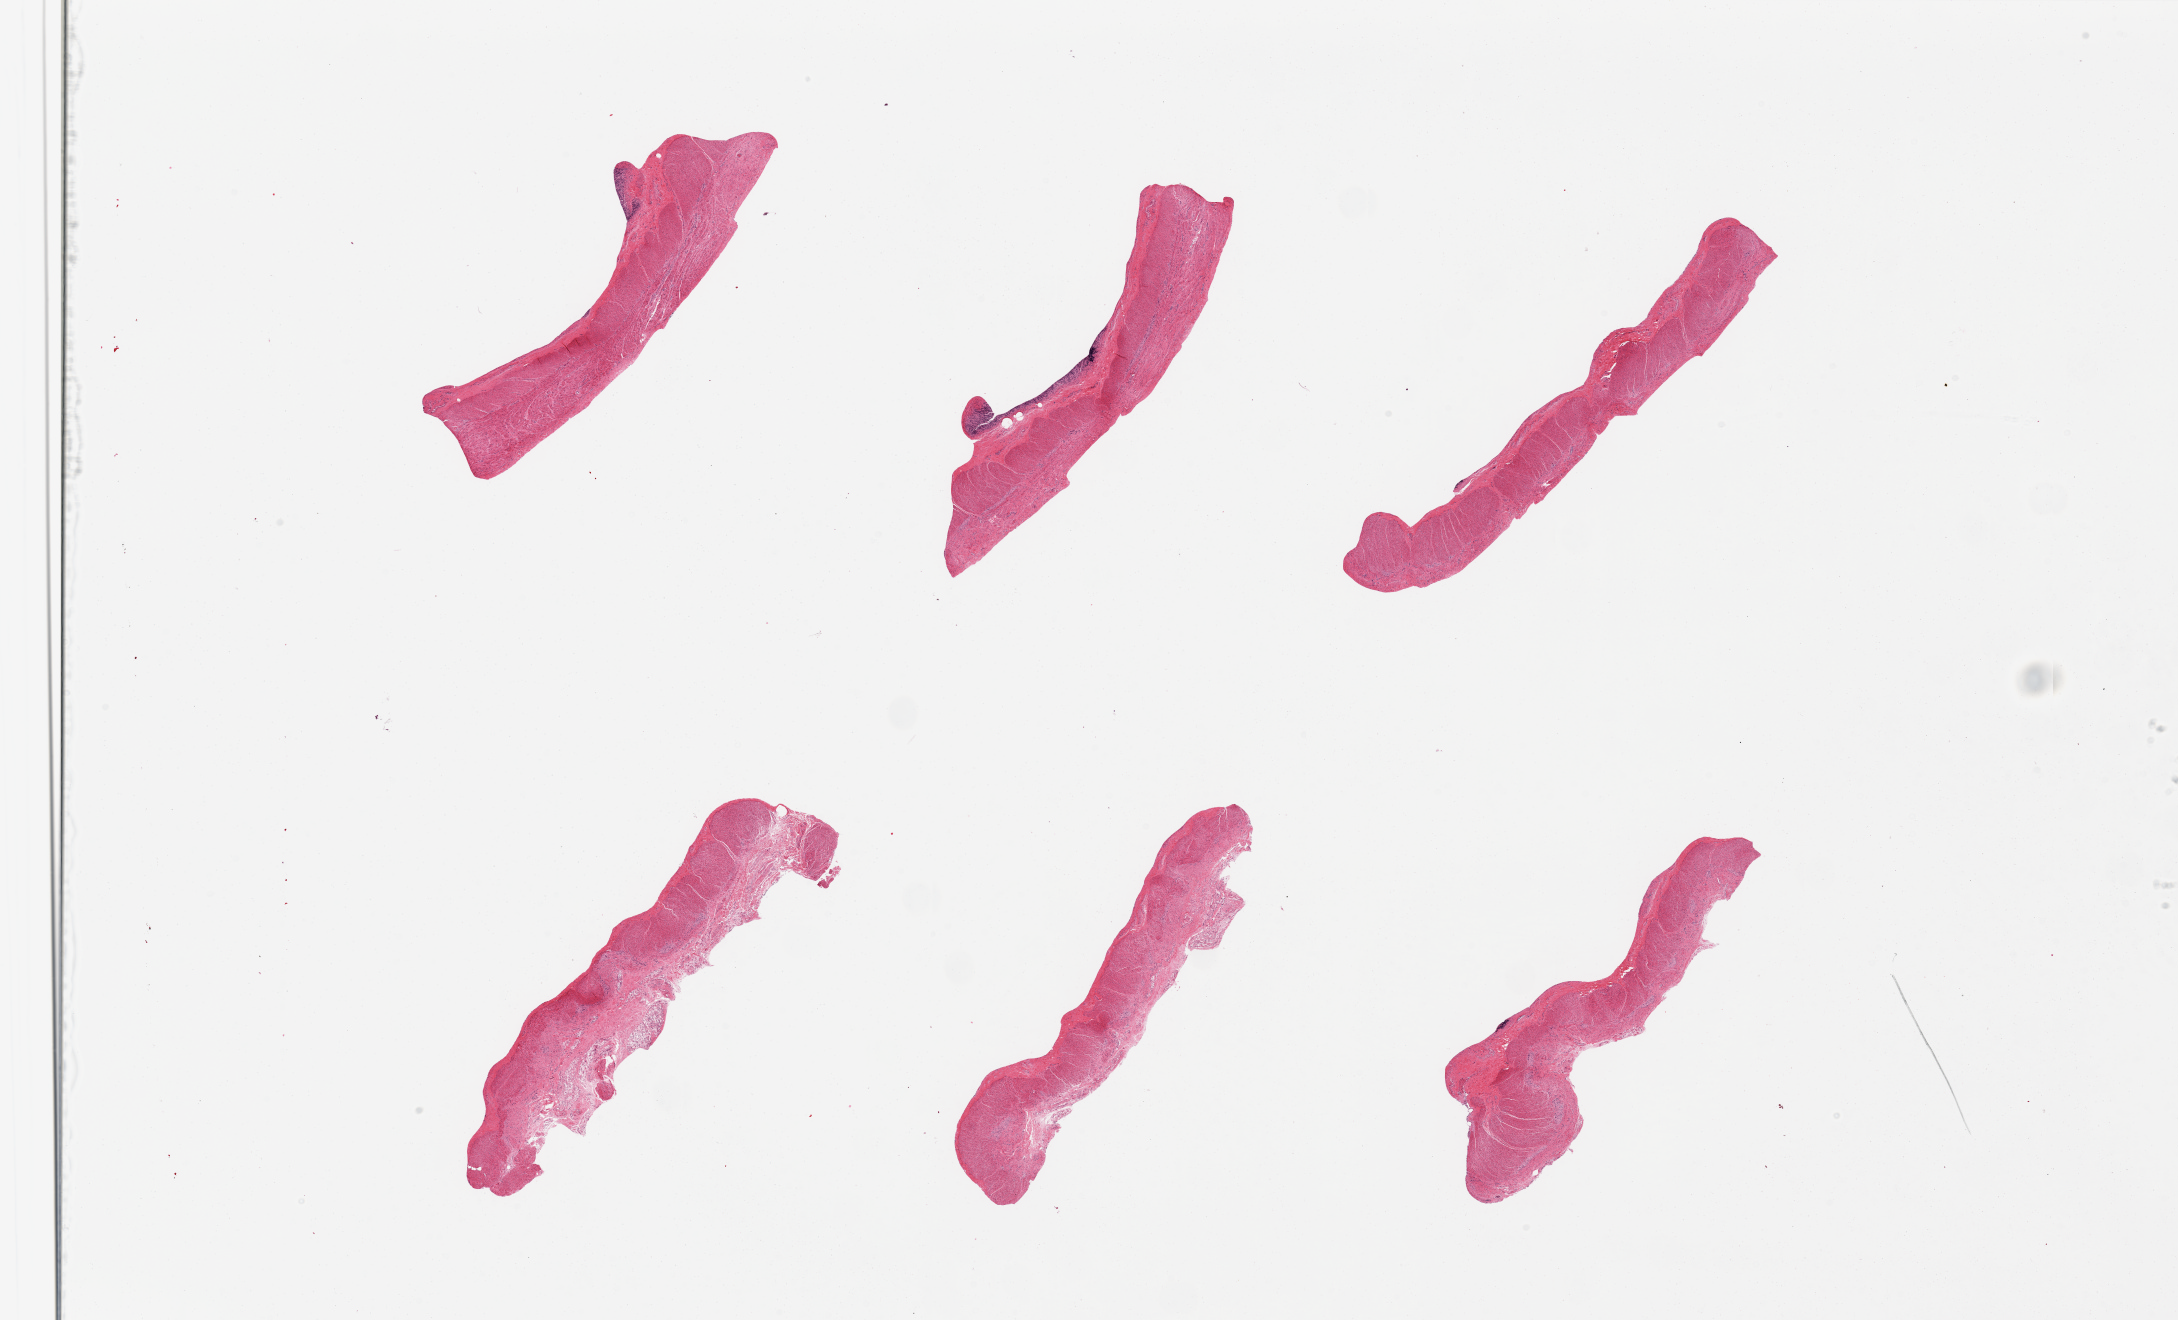
Haematoxylin and eosin whole-slide image, brightfield — whole scanned area (about 34.5 x 20.9 mm) shown as a low-resolution overview. Male donor.
Specimen: PAXgene-fixed paraffin-embedded (PFPE) section; sampled site (target tissue): sigmoid colon; donor tissue sample.